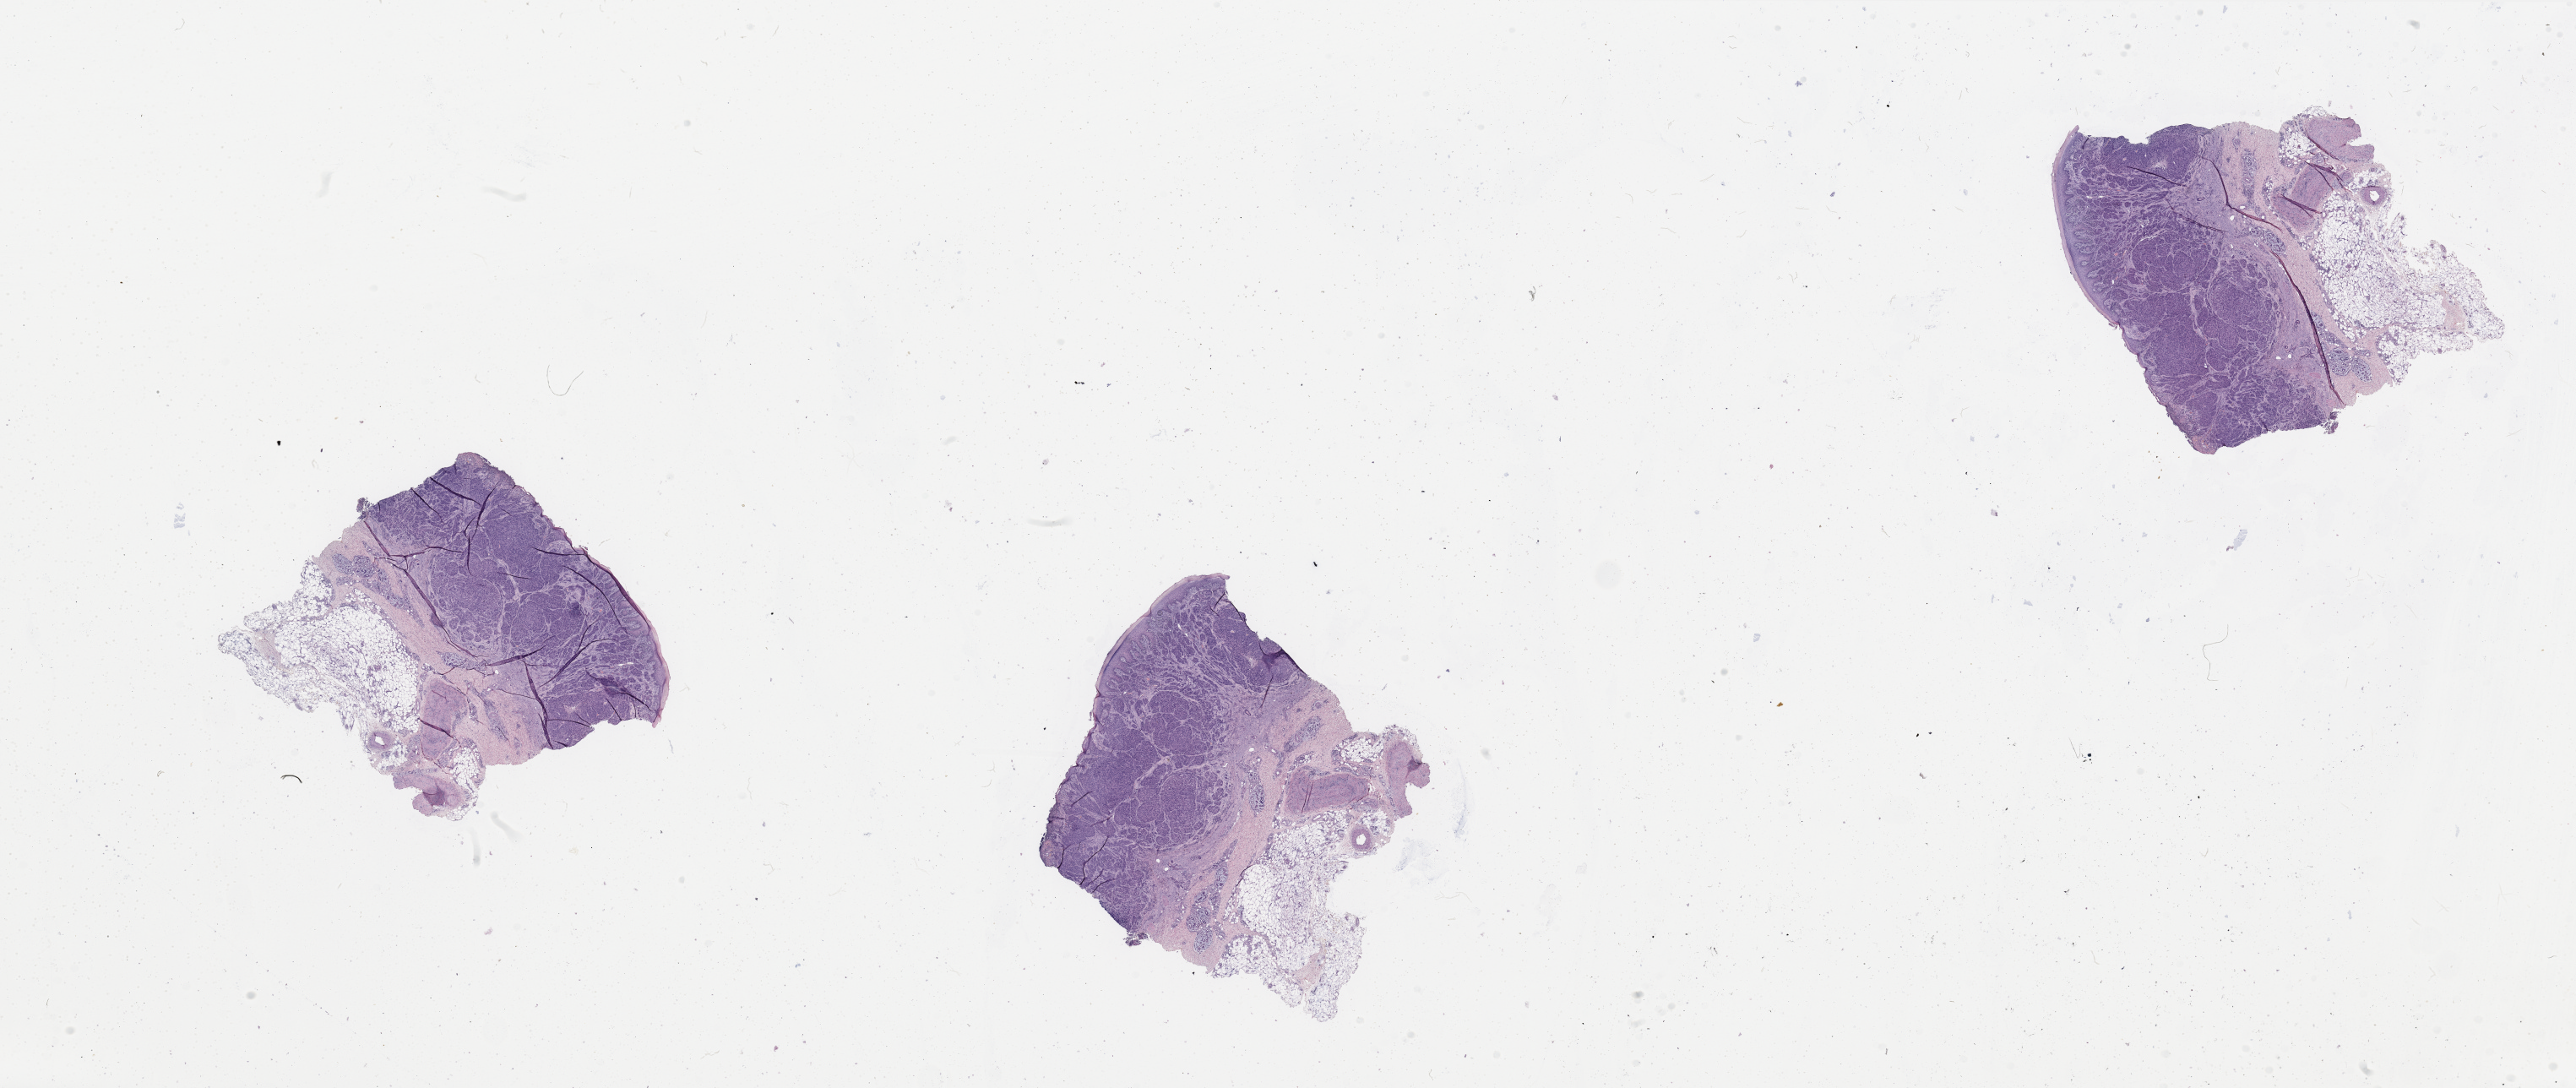
Whole-slide histology image, Hematoxylin and eosin (H&E) stained, shown as a low-resolution overview of the whole scanned area (about 48.2 x 20.4 mm). Tumour tissue sample, sampled site: skin. Female patient, aged 90 or older. Slide review estimates, as recorded: tumour nuclei 80%, necrosis 0%.
AJCC pathologic stage: IIC. Diagnosis: Malignant melanoma, NOS. Primary tumour site (as recorded): extremities.